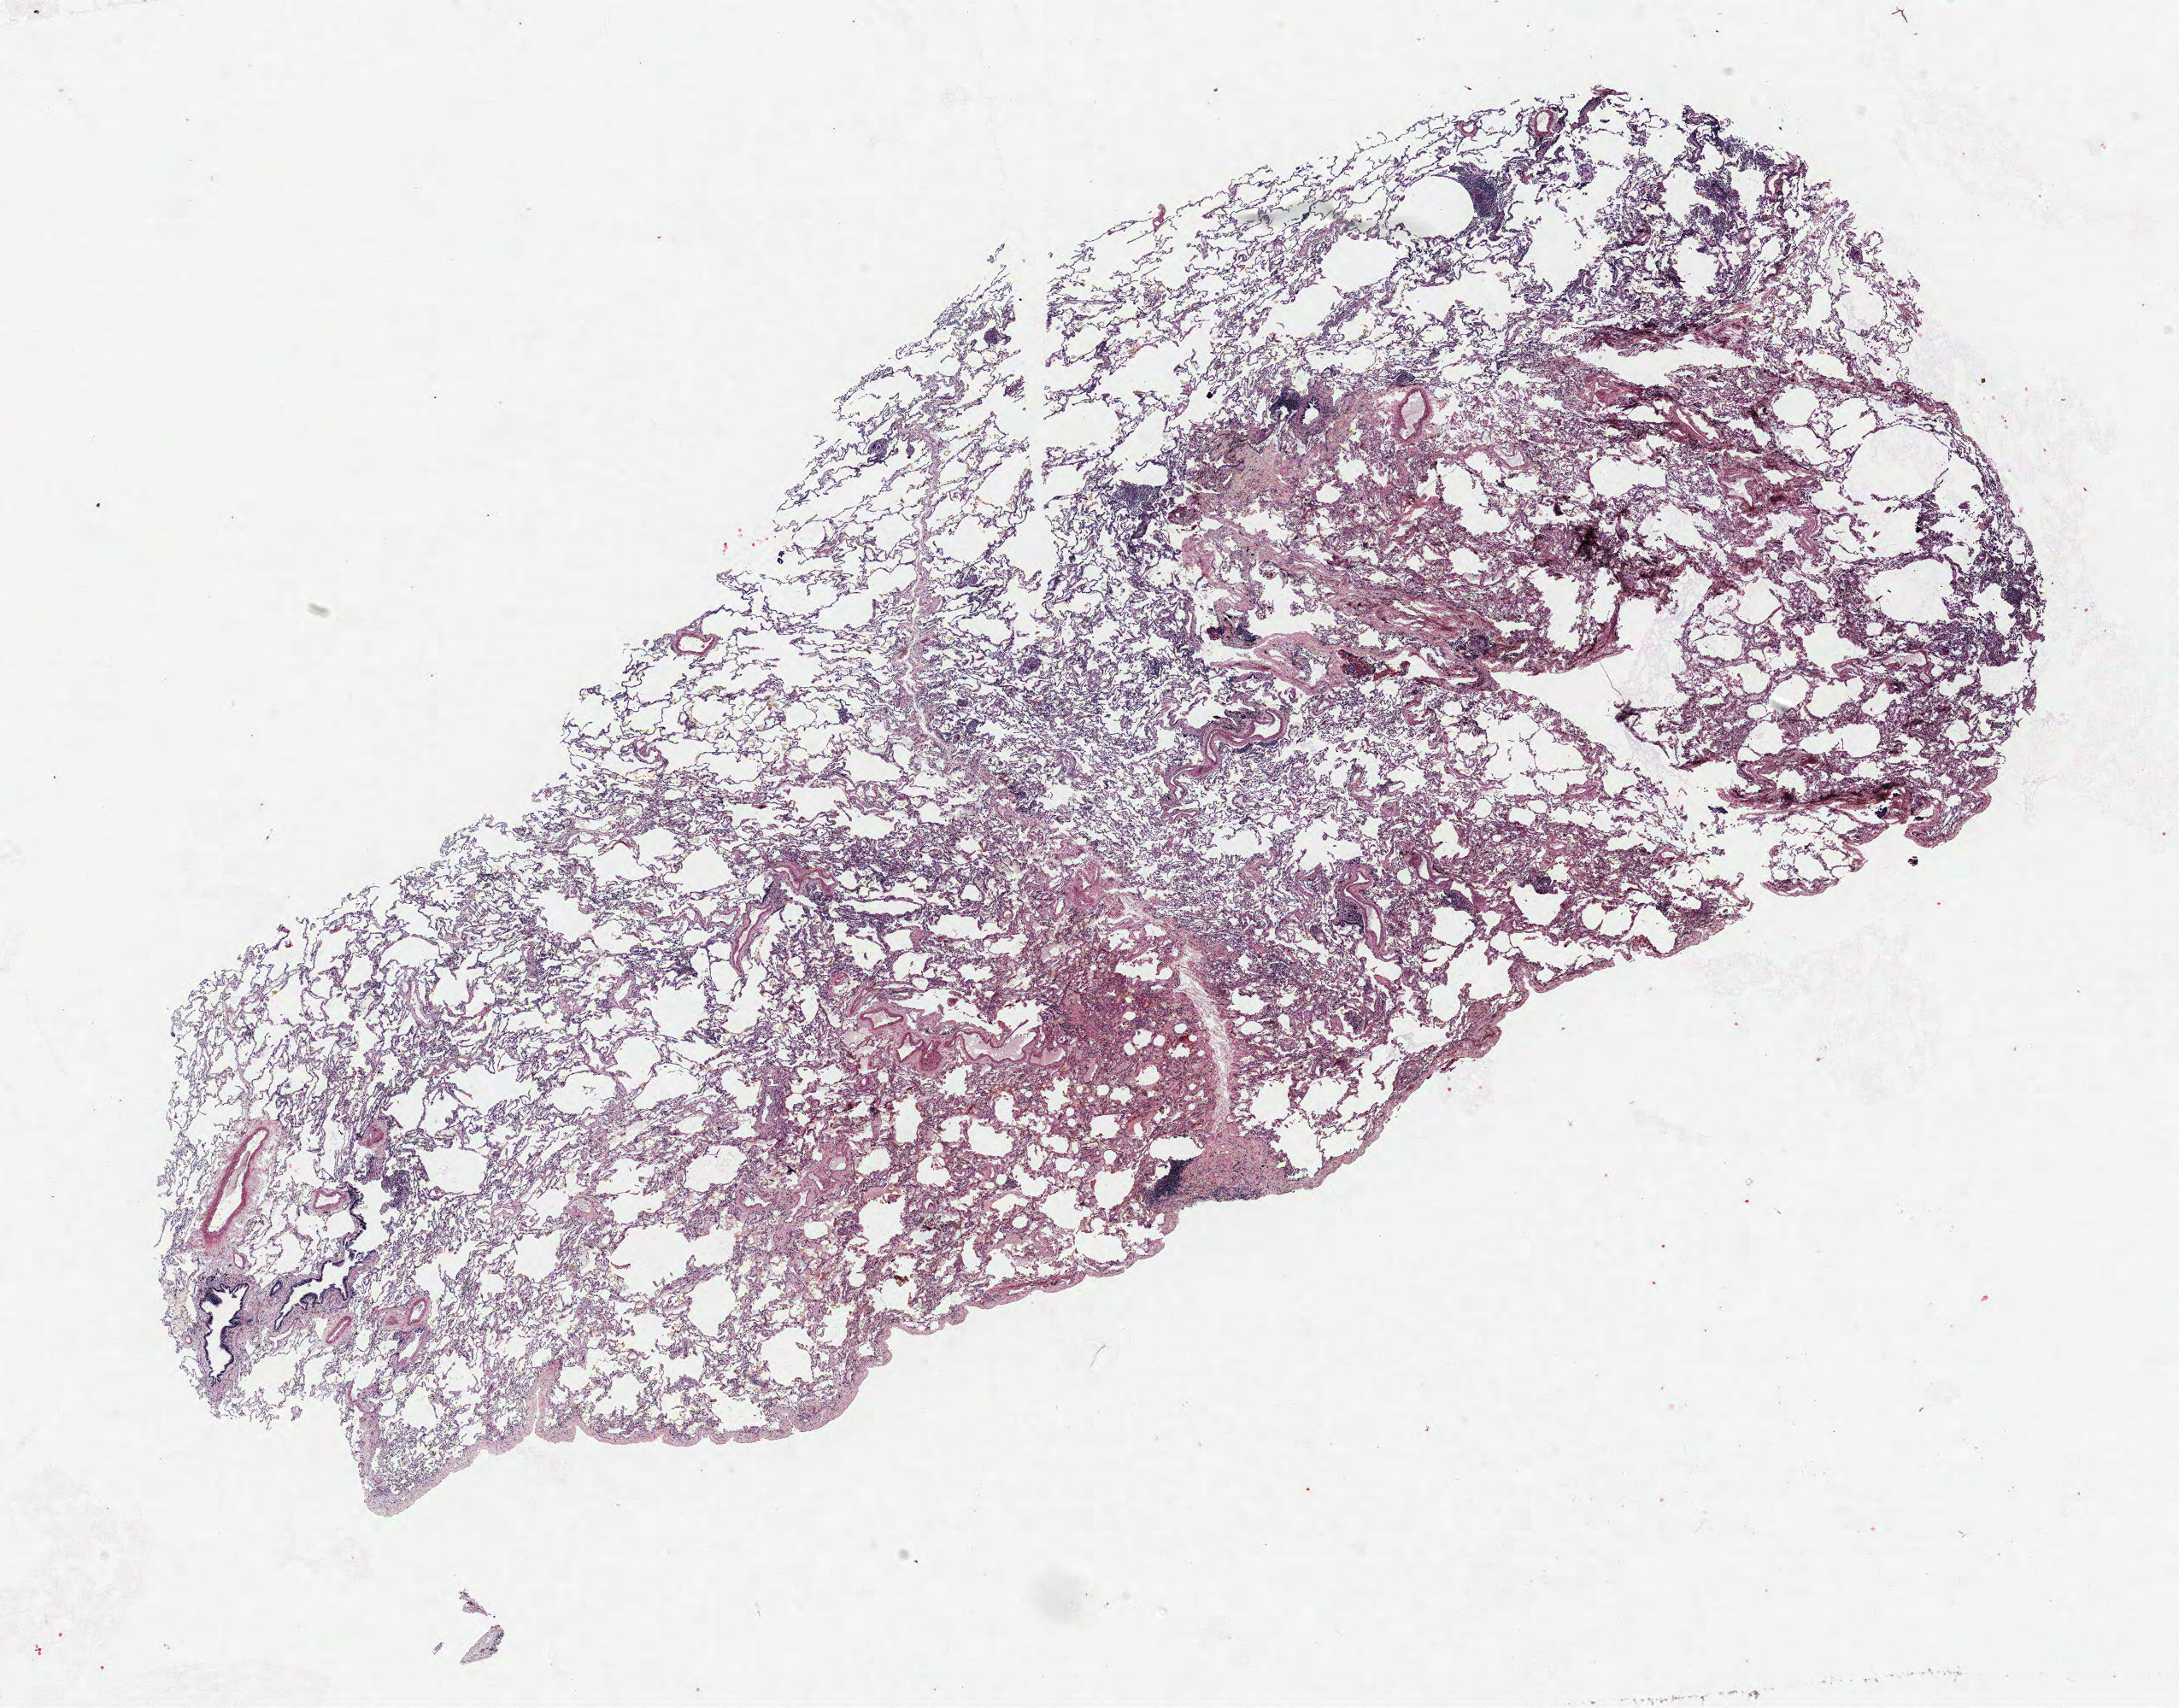
Whole-slide histology image, H&E — whole scanned area (about 20.4 x 16.0 mm) shown as a low-resolution overview; FFPE section; lung tissue. Male patient, aged 69 at enrolment. Former smoker at enrolment. Grade: moderately differentiated (G2).
Primary tumour location (clinical record): right upper lobe. Tumour size (pathology): 23 mm. ICD-O-3 topography: upper lobe of lung (C34.1). Participant's lung-cancer diagnosis: Adenocarcinoma, NOS. Stage (AJCC 6th edition): IA.